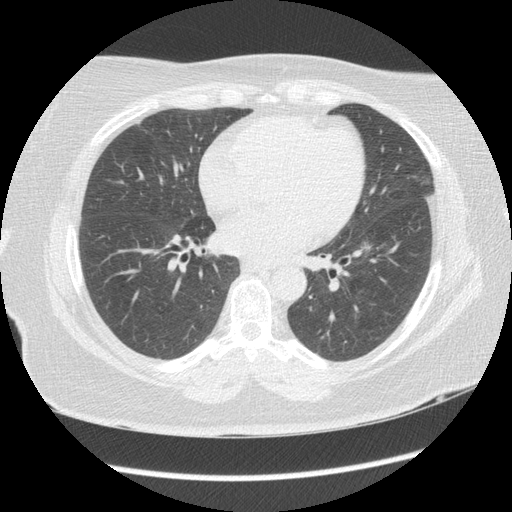
Axial slice from a low-dose chest CT screening exam. Third screening round (two years after baseline). Lung window (W 1500 / L -600 HU). Standard (soft-tissue) reconstruction kernel (STANDARD). 120 kVp. 512 × 512 image matrix, field of view 360 × 360 mm. Female participant, aged 65 years at enrolment. Current smoker at enrolment.
Expert-annotated lung lesion, bounding box <343,226,380,270> (left, top, right, bottom; pixels). Screening reader's record for this exam (one nodule recorded; not confirmed to be the boxed lesion): non-calcified nodule or mass ≥4 mm, left lower lobe, 130 × 90 mm, poorly defined margins, mixed attenuation, pre-existing on the prior screen: yes; interval growth: yes. Later outcome: lung cancer diagnosed 35 days after this screen — adenocarcinoma, NOS, left lower lobe, moderately differentiated (G2), stage IA (AJCC 6th edition), 12 mm at pathology.